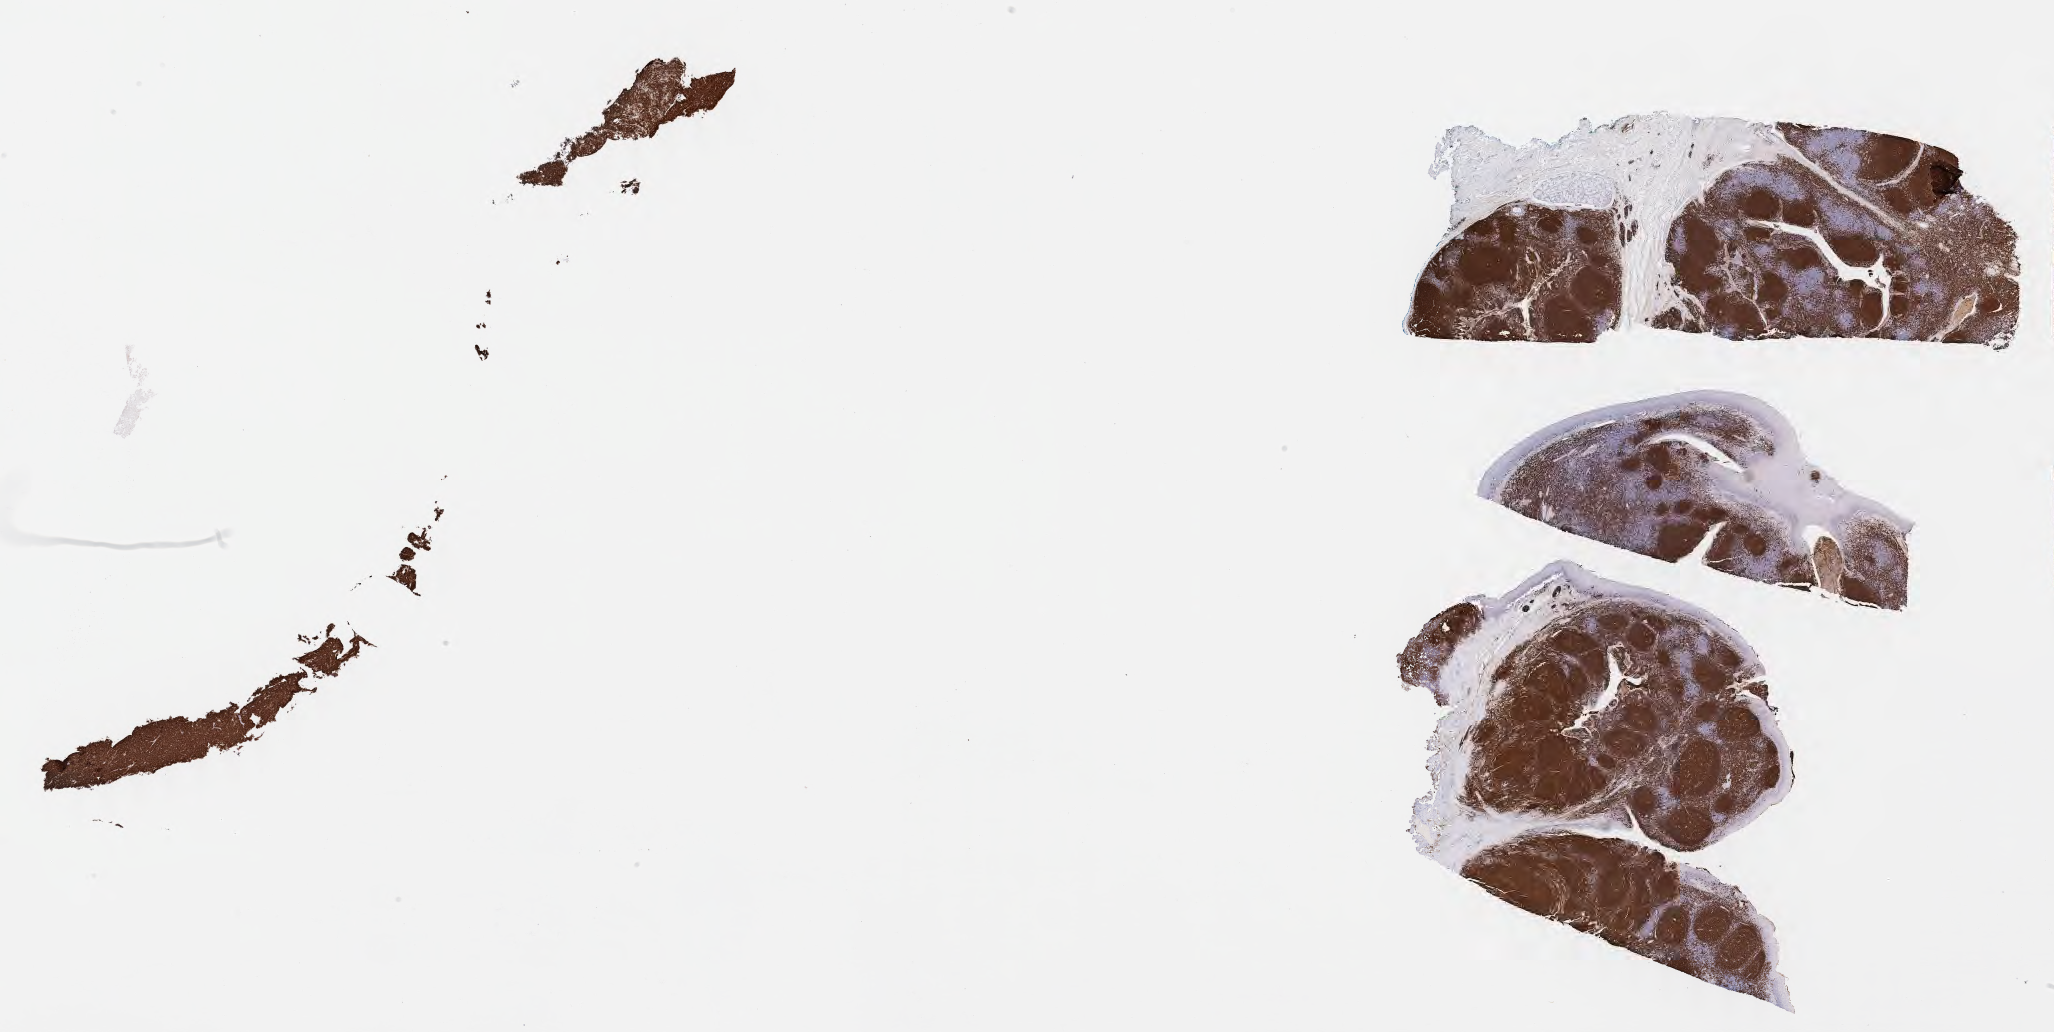
Whole-slide image, immunohistochemical stain for CD20 — low-resolution overview of the scanned area, about 33.2 x 16.7 mm, specimen: tumor tissue, site: cranium. Female patient; age at initial diagnosis 7 years.
- histologic diagnosis: Burkitt lymphoma, NOS